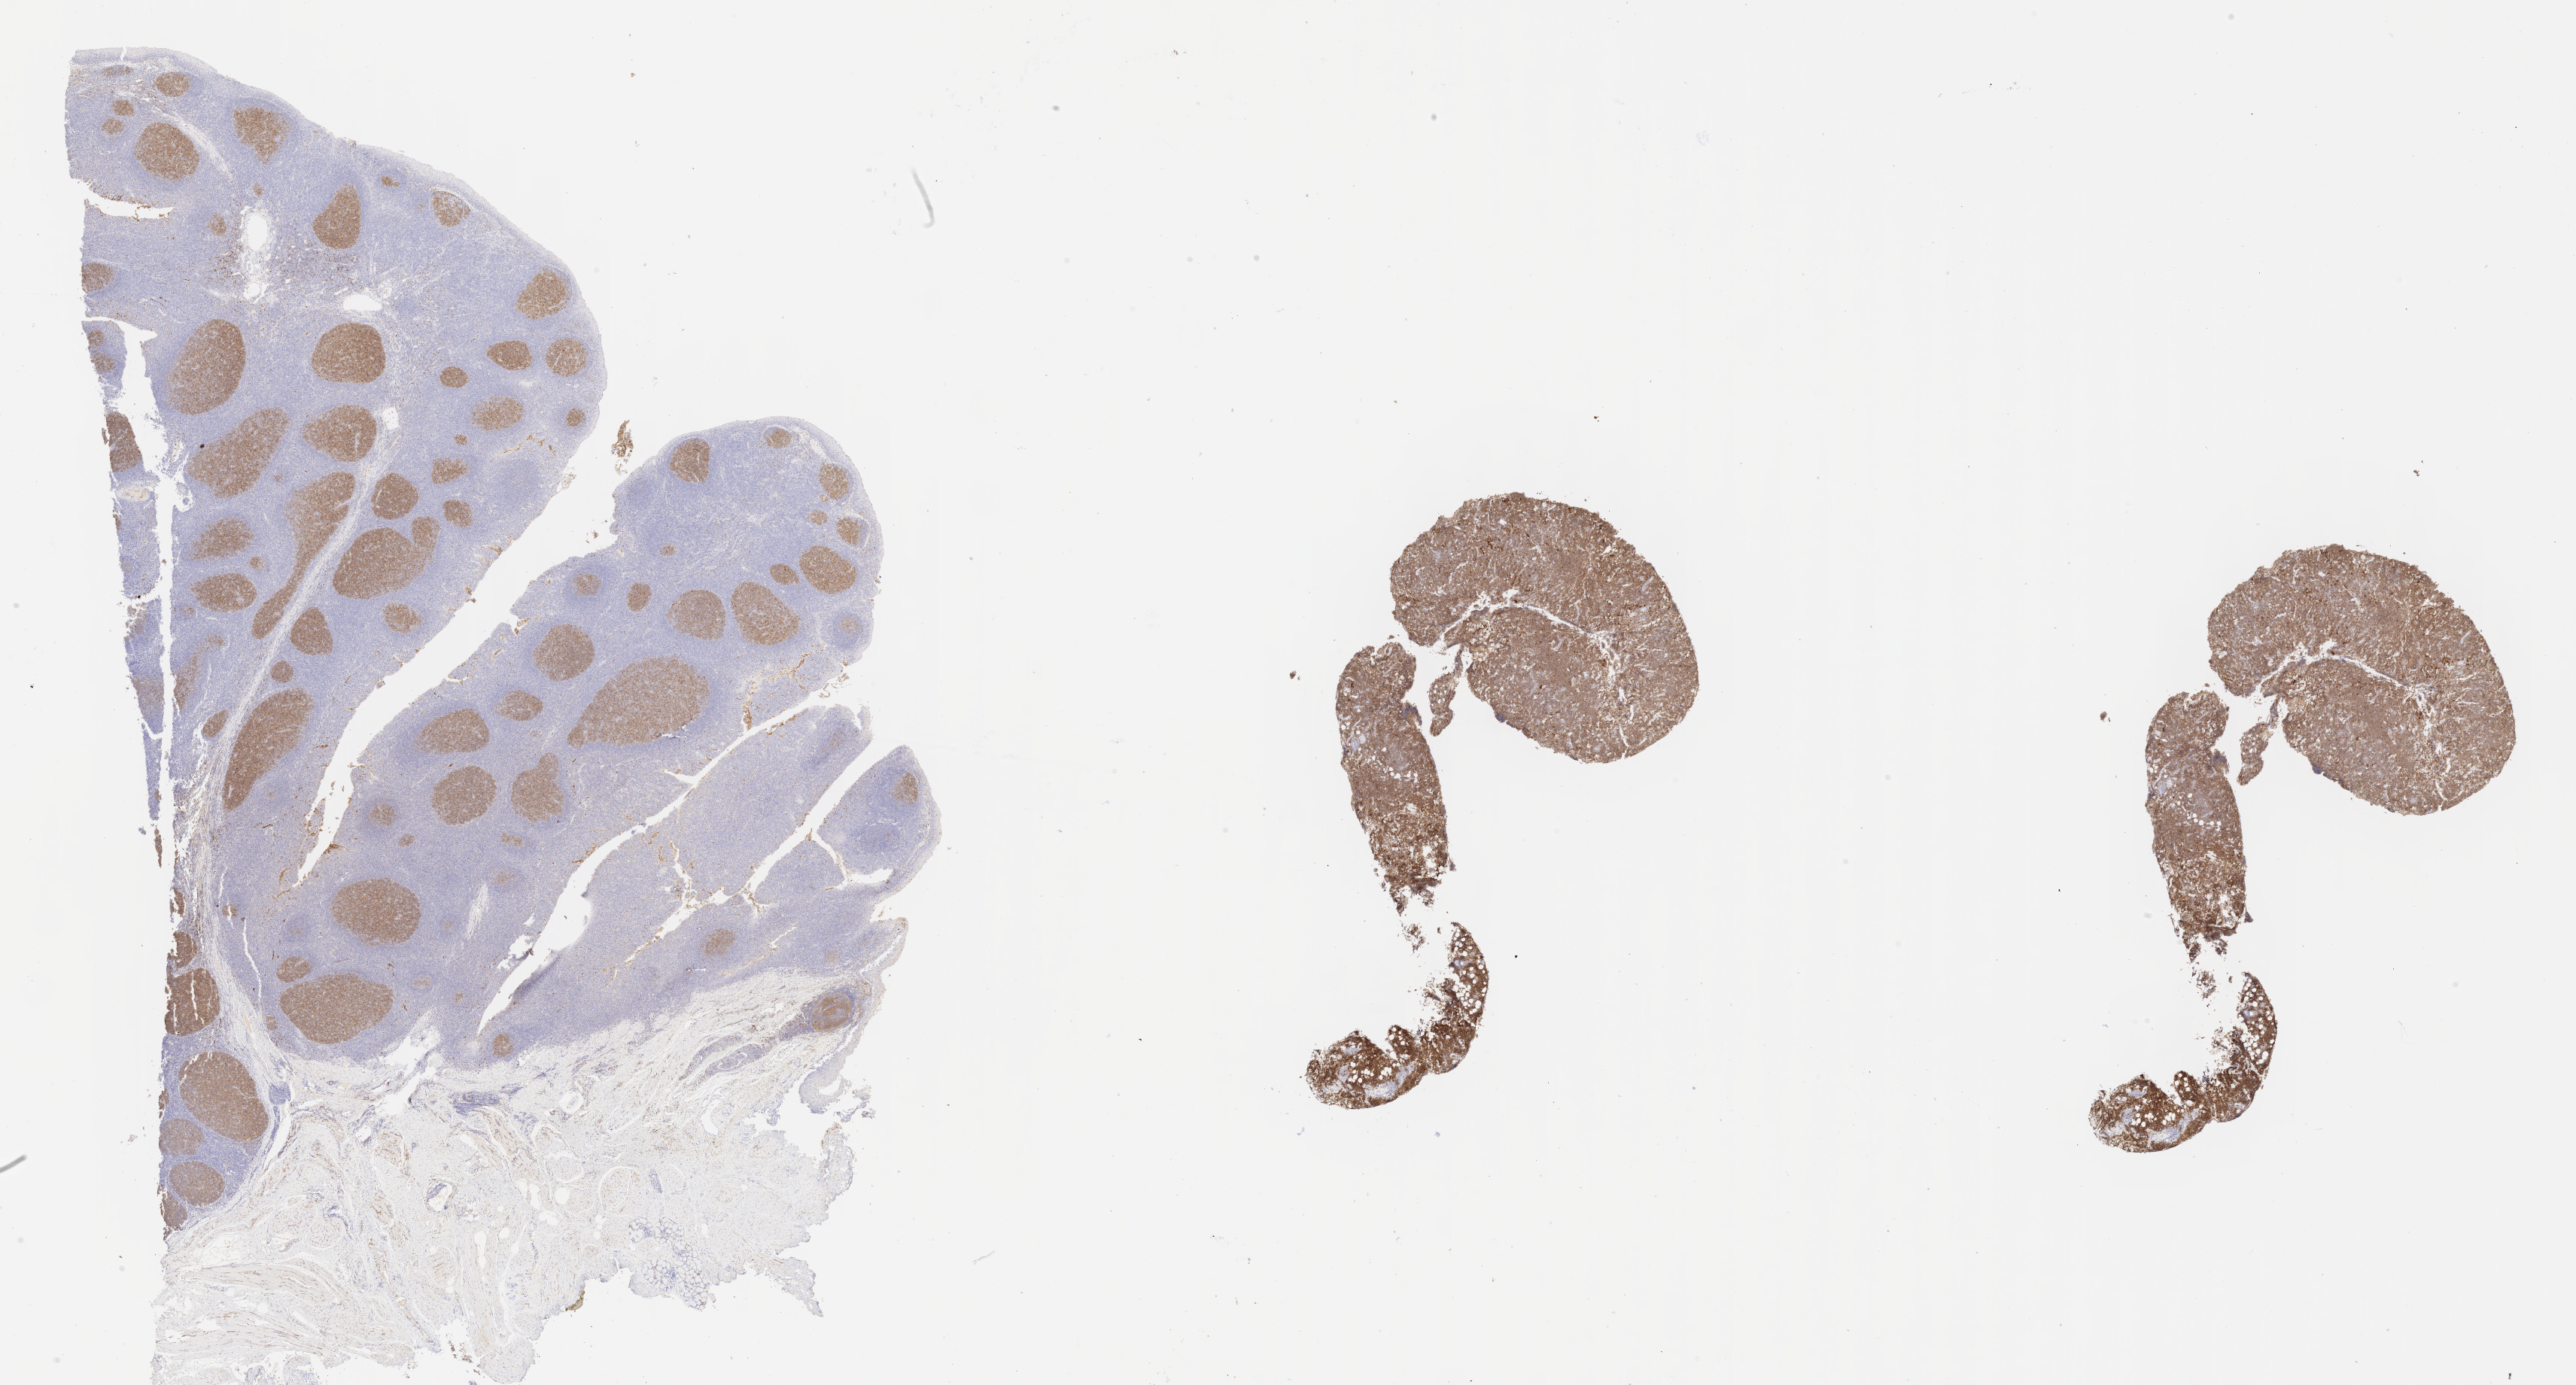
Whole-slide image, immunohistochemical stain for CD10, whole scanned area (about 27.7 x 14.9 mm) shown as a low-resolution overview, tumor tissue, site: head and neck. Patient: female, age 55 years.
• diagnosis: Burkitt lymphoma, NOS